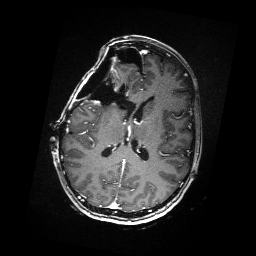
Brain MRI from a brain-tumour surgery series, one axial slice; slice 80 of 176 in the series (ordered by position); T1-weighted post-contrast; 256 × 256 image matrix, field of view 256 × 256 mm. Case-level facts recorded for this patient, not image findings: histopathology: Metastatic Carcinoma from Breast primary; tumour location: Right Frontal.
Annotated regions visible in this slice (expert manual segmentation):
- residual tumour: bounding box (x1, y1, x2, y2) in pixels: (110, 70, 114, 73)